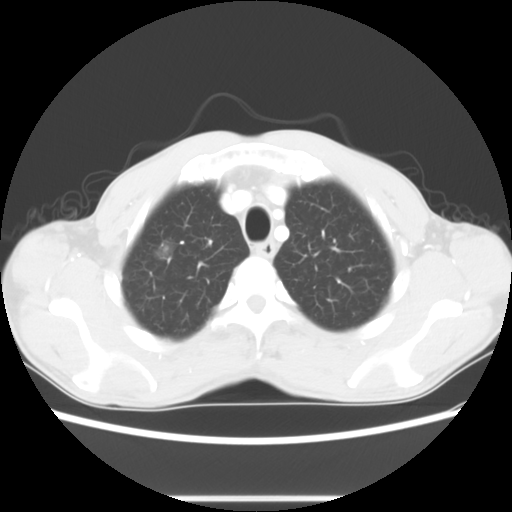
Chest CT, one axial slice. Slice 60 of 73 in the series (ordered by position). Reconstruction kernel STANDARD. 100 kVp. Lung window (W 1500 / L -600 HU). 5 mm slice thickness. 512 × 512 image matrix. Patient: male, 54 years. From the clinical record (not read from this slice): clinical TNM (as recorded): T1a N0 M0.
Annotated regions visible in this slice (rectangle marked by the reading radiologist):
- lung tumour (recorded histology: adenocarcinoma): bounding box [x1, y1, x2, y2] px = [148, 235, 187, 268]